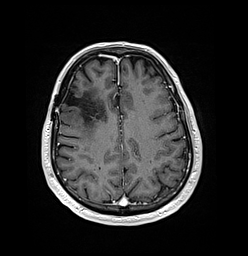
Brain MRI from a brain-tumour surgery series, one axial slice. Position 54 of 176 along the scan axis. T1-weighted post-contrast. 1 mm slice thickness. 248 × 256 image matrix, field of view 242 × 250 mm. From the clinical record (not read from this slice): histopathology: Oligodendroglioma; WHO grade: 3; IDH mutation: yes; tumour location: Right Frontal.
Annotated regions visible in this slice (expert manual segmentation):
- previous resection cavity: bounding box <63,91,83,106> (left, top, right, bottom; pixels)